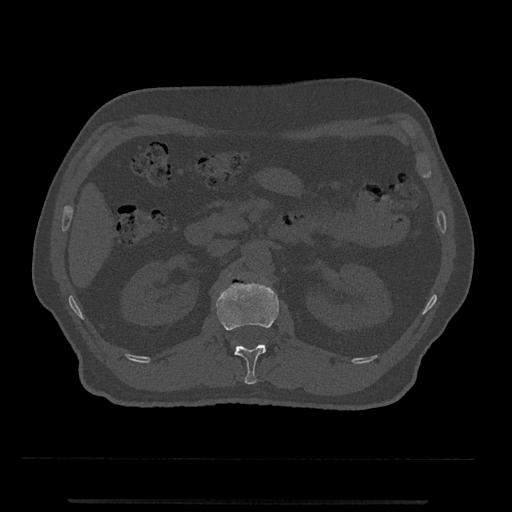
CT including the spine, one axial slice; position 318 of 797 along the scan axis; reconstruction kernel Br40s/3; bone window (W 1800 / L 400 HU); 512 × 512 image matrix, field of view 419 × 419 mm. Patient: male, 63 years. Case-level facts recorded for this patient, not image findings: primary cancer: prostate.
Annotated regions visible in this slice (semi-automatically segmented with operator editing):
- L1 vertebra: box from (x=216, y=283) to (x=279, y=385) px
- L2 vertebra: (x=228, y=274)–(x=230, y=277)